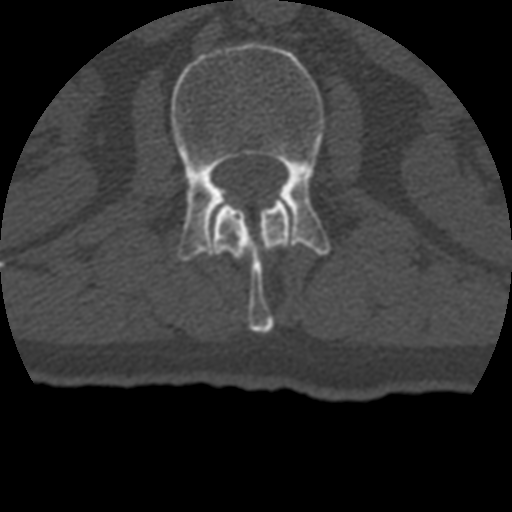
CT including the spine, one axial slice; slice 128 of 399 in the series (ordered by position); 120 kVp; bone window (W 1800 / L 400 HU); 1.25 mm slice thickness; 512 × 512 image matrix, field of view 160 × 160 mm. Patient age 69 years. From the clinical record (not read from this slice): primary cancer: prostate.
Structures marked on this image (semi-automatic segmentation, software-assisted and operator-edited):
- L1 vertebra: box from (x=211, y=198) to (x=292, y=333) px
- L2 vertebra: (x=171, y=43)–(x=331, y=261)